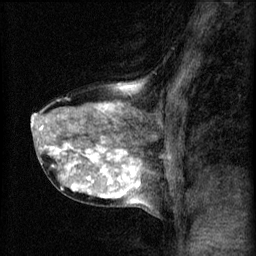
Breast MRI (dynamic contrast-enhanced), one sagittal slice. Slice 33 of 60 in the series (ordered by position). 3 images stored at this slice position (order not interpretable as contrast timing). 1.5 T. TE 4.2 ms, TR 8.2 ms. 2 mm slice thickness. 256 × 256 image matrix, field of view 180 × 180 mm. Patient: female, 40 years.
Outlined on this slice (semi-automatically segmented with operator editing):
- analysis volume of interest (the breast-tissue region the enhancement analysis was run in; not a lesion): bounding box [x1, y1, x2, y2] px = [31, 80, 167, 211]
- tumour enhancement mask (voxels above the 70 % enhancement threshold inside the analysis volume of interest): [32, 84, 143, 205]